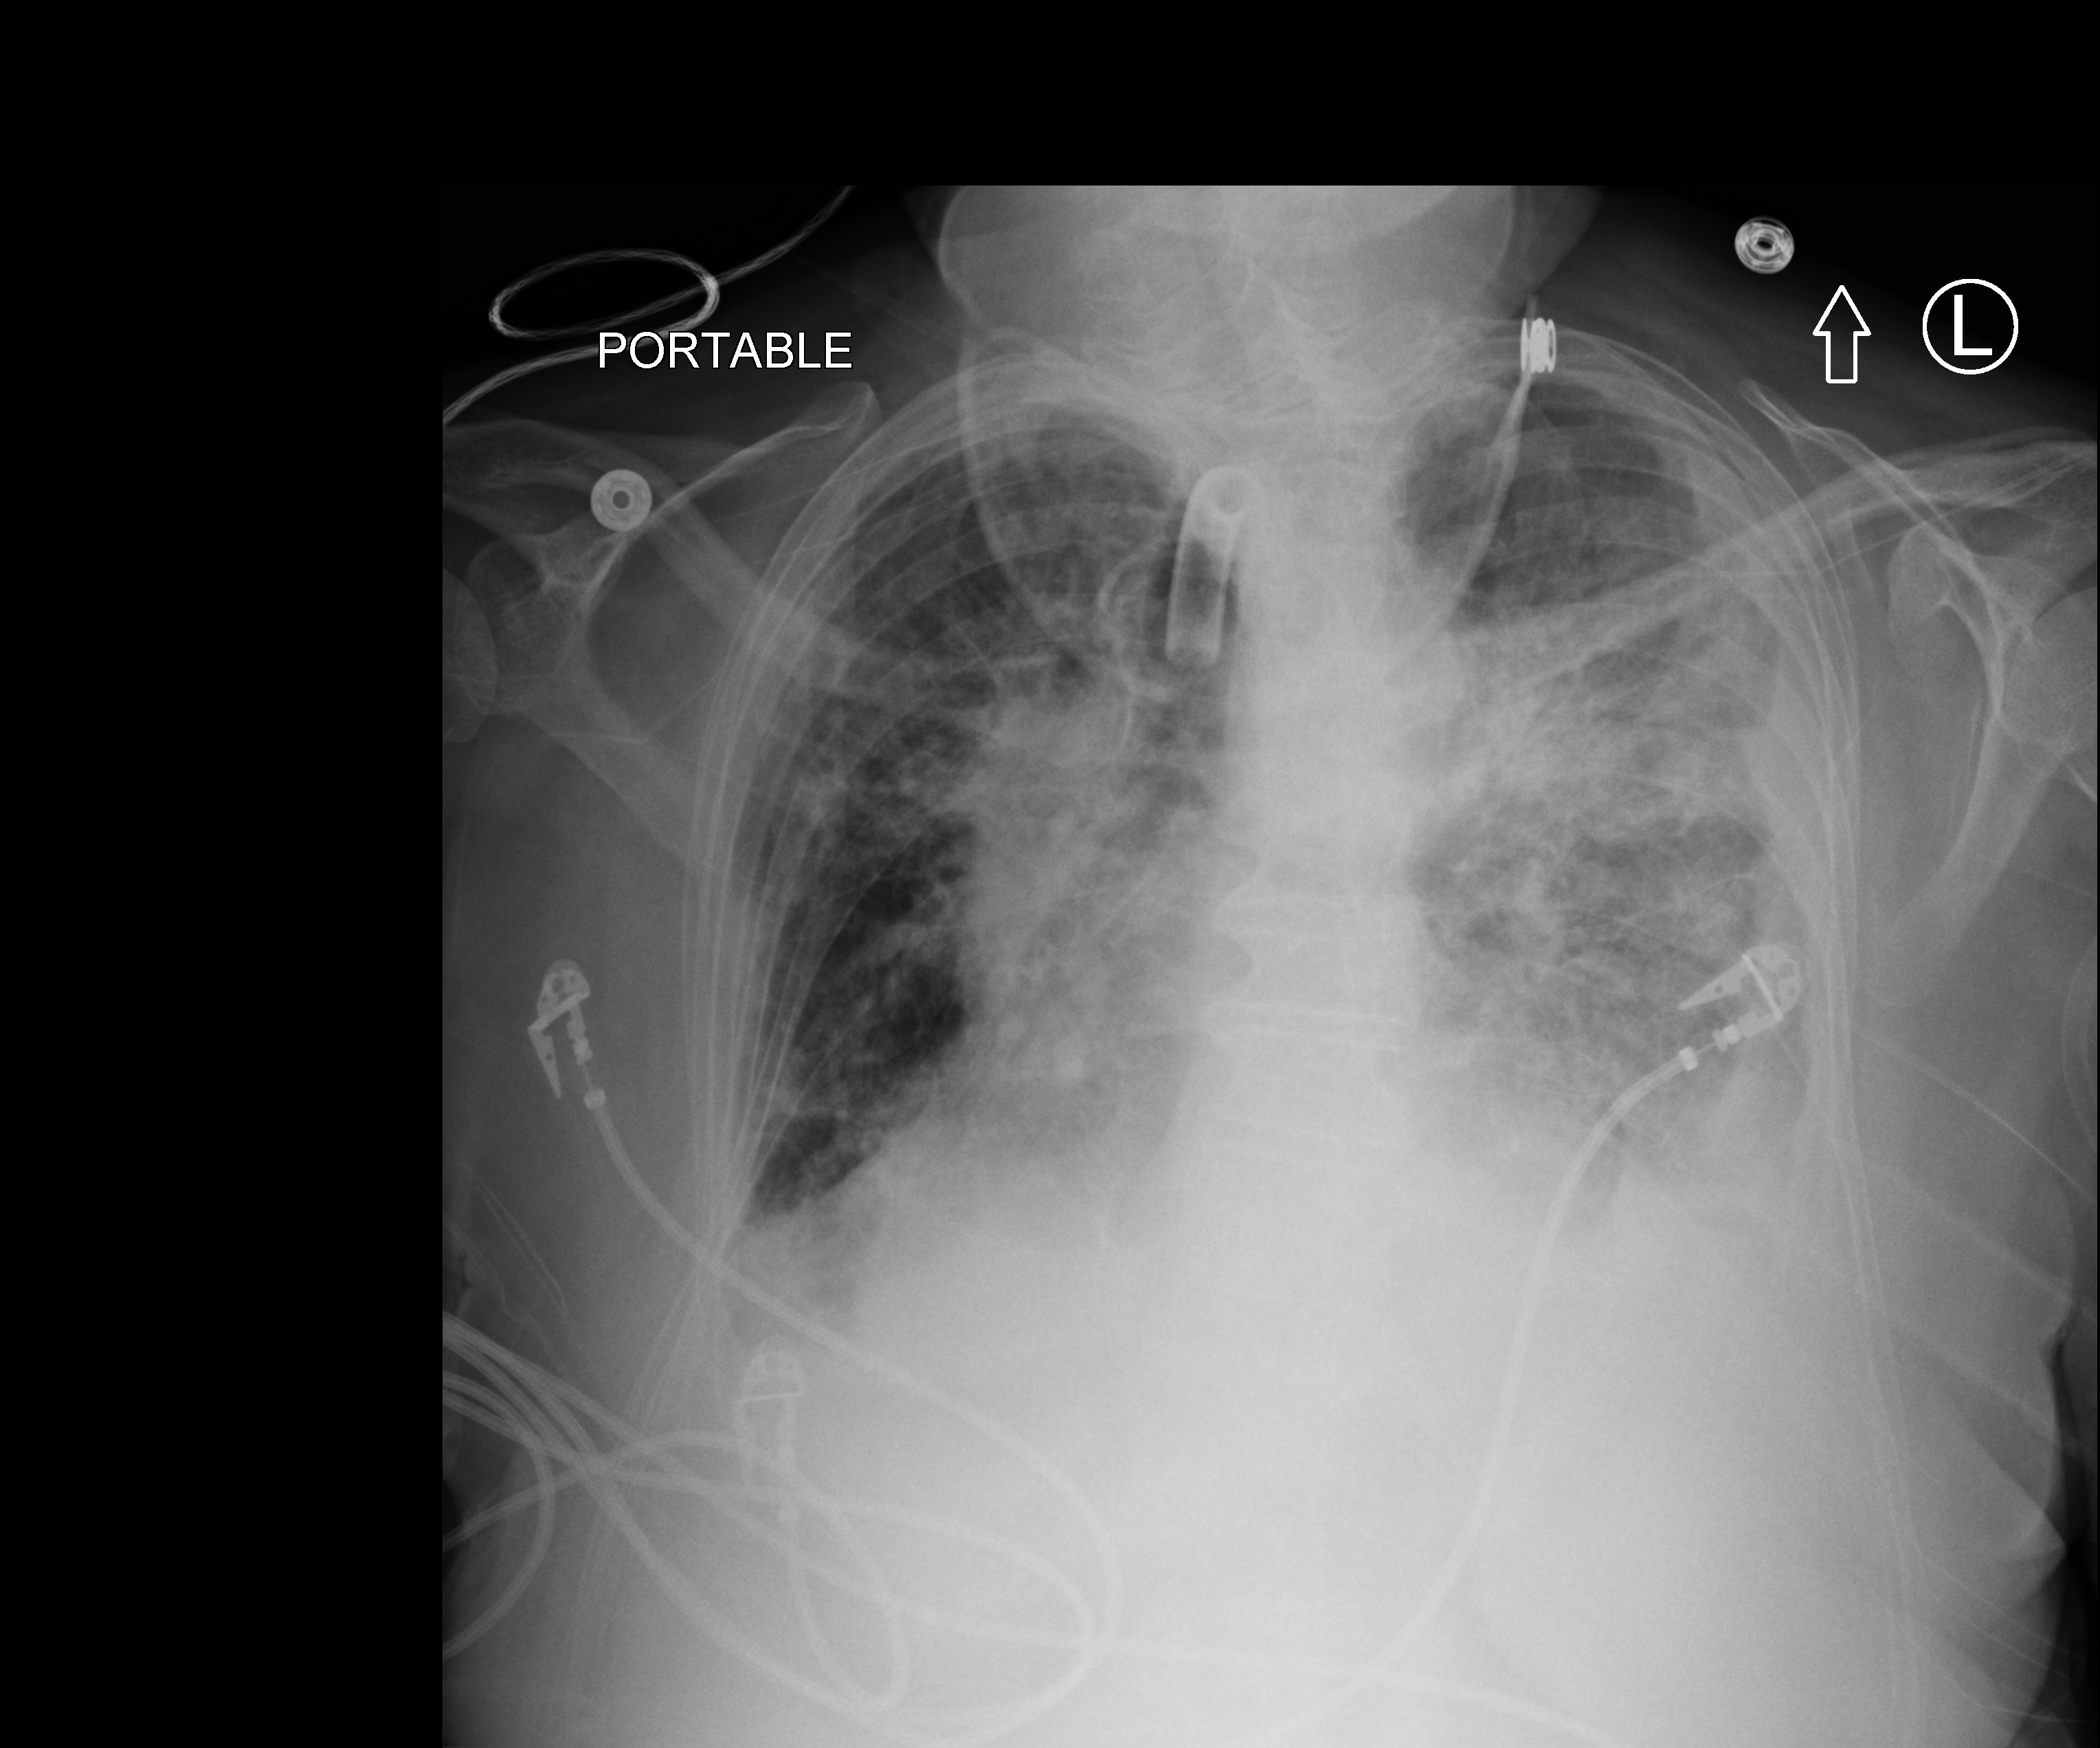
Chest X-ray (portable). Patient hospitalised with COVID-19; female, aged 75–90 years.
From the hospital-stay record, not from the radiograph (when in the stay this image was taken is not recorded): length of hospital stay: 70 days; chronic kidney disease (admission record): no; smoking status (admission record): former.